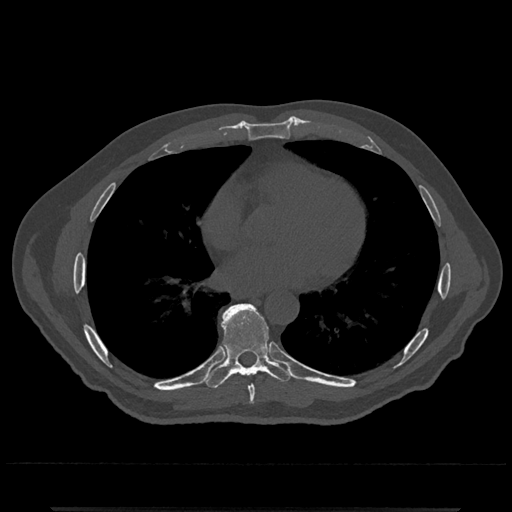
CT including the spine, one axial slice. Slice 682 of 797 in the series (ordered by position). 120 kVp. Bone window (W 1800 / L 400 HU). 512 × 512 image matrix, field of view 393 × 393 mm. Male patient, age 67 years. From the clinical record (not read from this slice): primary cancer: prostate.
Annotated regions visible in this slice (semi-automatic segmentation, software-assisted and operator-edited):
- T7 vertebra: bounding box <248,385,255,404> (left, top, right, bottom; pixels)
- T8 vertebra: <202,304,296,389>